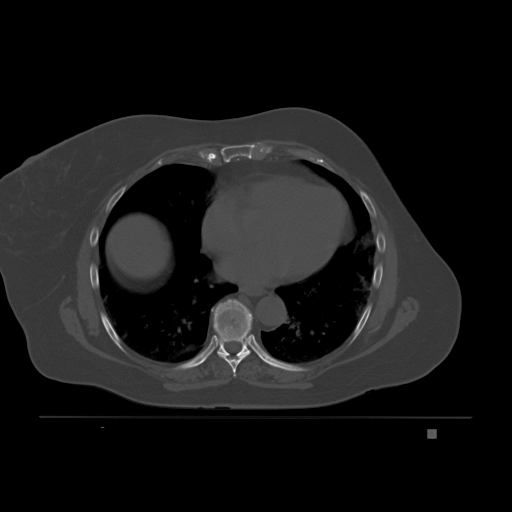
CT including the spine, one axial slice. Position 123 of 221 along the scan axis. Bone window (W 1800 / L 400 HU). 512 × 512 image matrix, field of view 474 × 474 mm. Female patient, age 63 years. Case-level facts recorded for this patient, not image findings: primary cancer: breast.
Structures marked on this image (semi-automatically segmented with operator editing):
- T7 vertebra: bounding box <212,309,250,377> (left, top, right, bottom; pixels)
- T8 vertebra: <211,299,253,356>